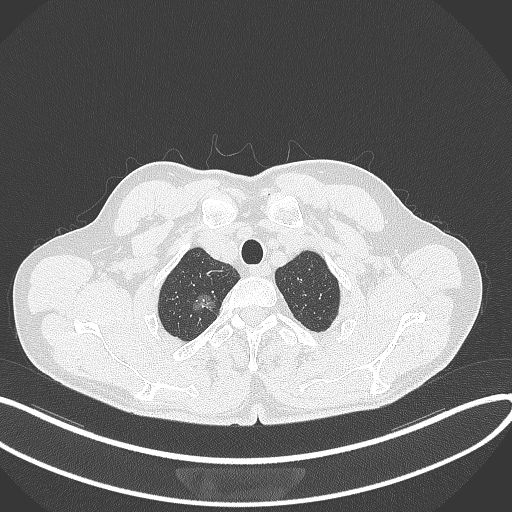
Chest CT, one axial slice. Position 347 of 407 along the scan axis. Reconstruction kernel B70f. 120 kVp. Lung window (W 1500 / L -600 HU). 512 × 512 image matrix. Patient: male, 58 years. From the clinical record (not read from this slice): clinical TNM (as recorded): T1c N0 M0; histopathological grade: G1-2.
Outlined on this slice (rectangle marked by the reading radiologist):
- lung tumour (recorded histology: adenocarcinoma): box from (x=185, y=289) to (x=223, y=319) px